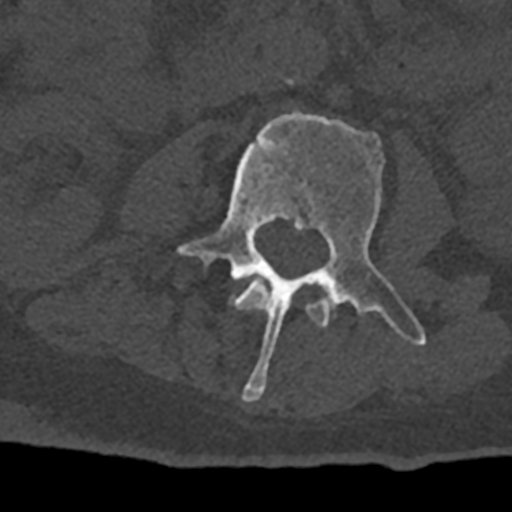
CT including the spine, one axial slice. Slice 324 of 797 in the series (ordered by position). 120 kVp. Bone window (W 1800 / L 400 HU). 512 × 512 image matrix, field of view 160 × 160 mm. Patient: male, 74 years. Case-level facts recorded for this patient, not image findings: primary cancer: renal; vertebrae with lytic lesions (as recorded): T10, L1, L2, L3, L4, L5.
Structures marked on this image (semi-automatic segmentation, software-assisted and operator-edited):
- L2 vertebra: bounding box (x1, y1, x2, y2) in pixels: (231, 281, 329, 328)
- L3 vertebra: (176, 111, 426, 401)